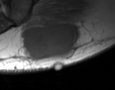
MRI of an extremity soft-tissue mass, one axial slice. Position 17 of 35 along the scan axis. MR volume resampled by the dataset authors to the PET/CT grid (not the native acquisition matrix). 3.27 mm slice thickness. 115 × 90 image matrix. Male patient. Case-level facts recorded for this patient, not image findings: histological type: pleiomorphic leiomyosarcoma; grade: high; site of the primary tumour: left buttock.
Outlined on this slice (expert contour drawn on MRI and transferred to this co-registered scan by the dataset authors):
- gross tumour volume including surrounding oedema: bounding box [x1, y1, x2, y2] px = [23, 21, 81, 60]
- gross tumour volume (mass): [23, 21, 81, 60]